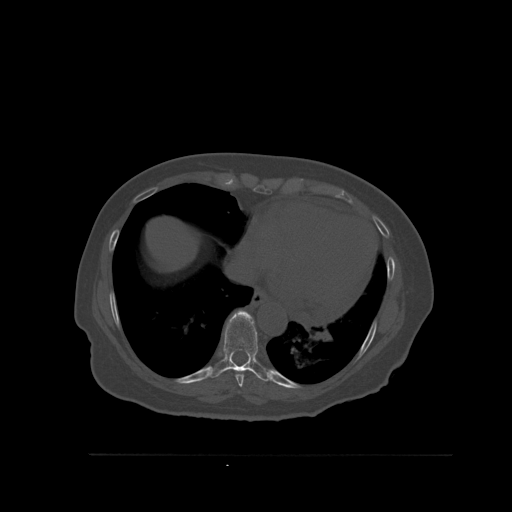
CT including the spine, one axial slice; bone window (W 1800 / L 400 HU); 1.5 mm slice thickness; 512 × 512 image matrix. Patient: female, 73 years. Case-level facts recorded for this patient, not image findings: primary cancer: breast.
Outlined on this slice (semi-automatically segmented with operator editing):
- T8 vertebra: bounding box (x1, y1, x2, y2) in pixels: (235, 370, 249, 387)
- T9 vertebra: (210, 310, 272, 382)